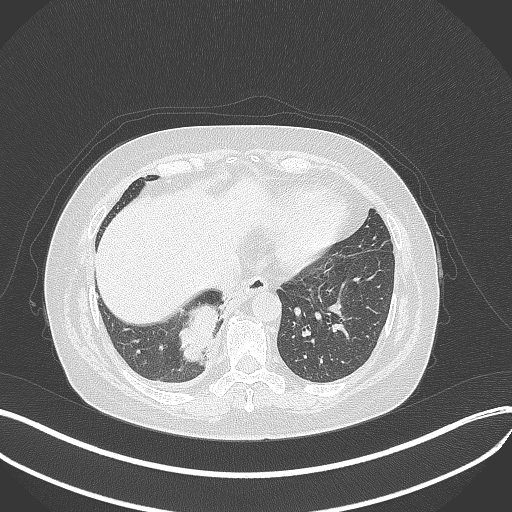
Chest CT, one axial slice. Reconstruction kernel B70f. Lung window (W 1500 / L -600 HU). 512 × 512 image matrix, field of view 400 × 400 mm. Patient: female, 56 years. Case-level facts recorded for this patient, not image findings: clinical TNM (as recorded): T2b N1 M0; histopathological grade: G3.
Outlined on this slice (bounding box drawn by a radiologist):
- lung tumour (recorded histology: small cell carcinoma): bounding box <173,300,219,364> (left, top, right, bottom; pixels)